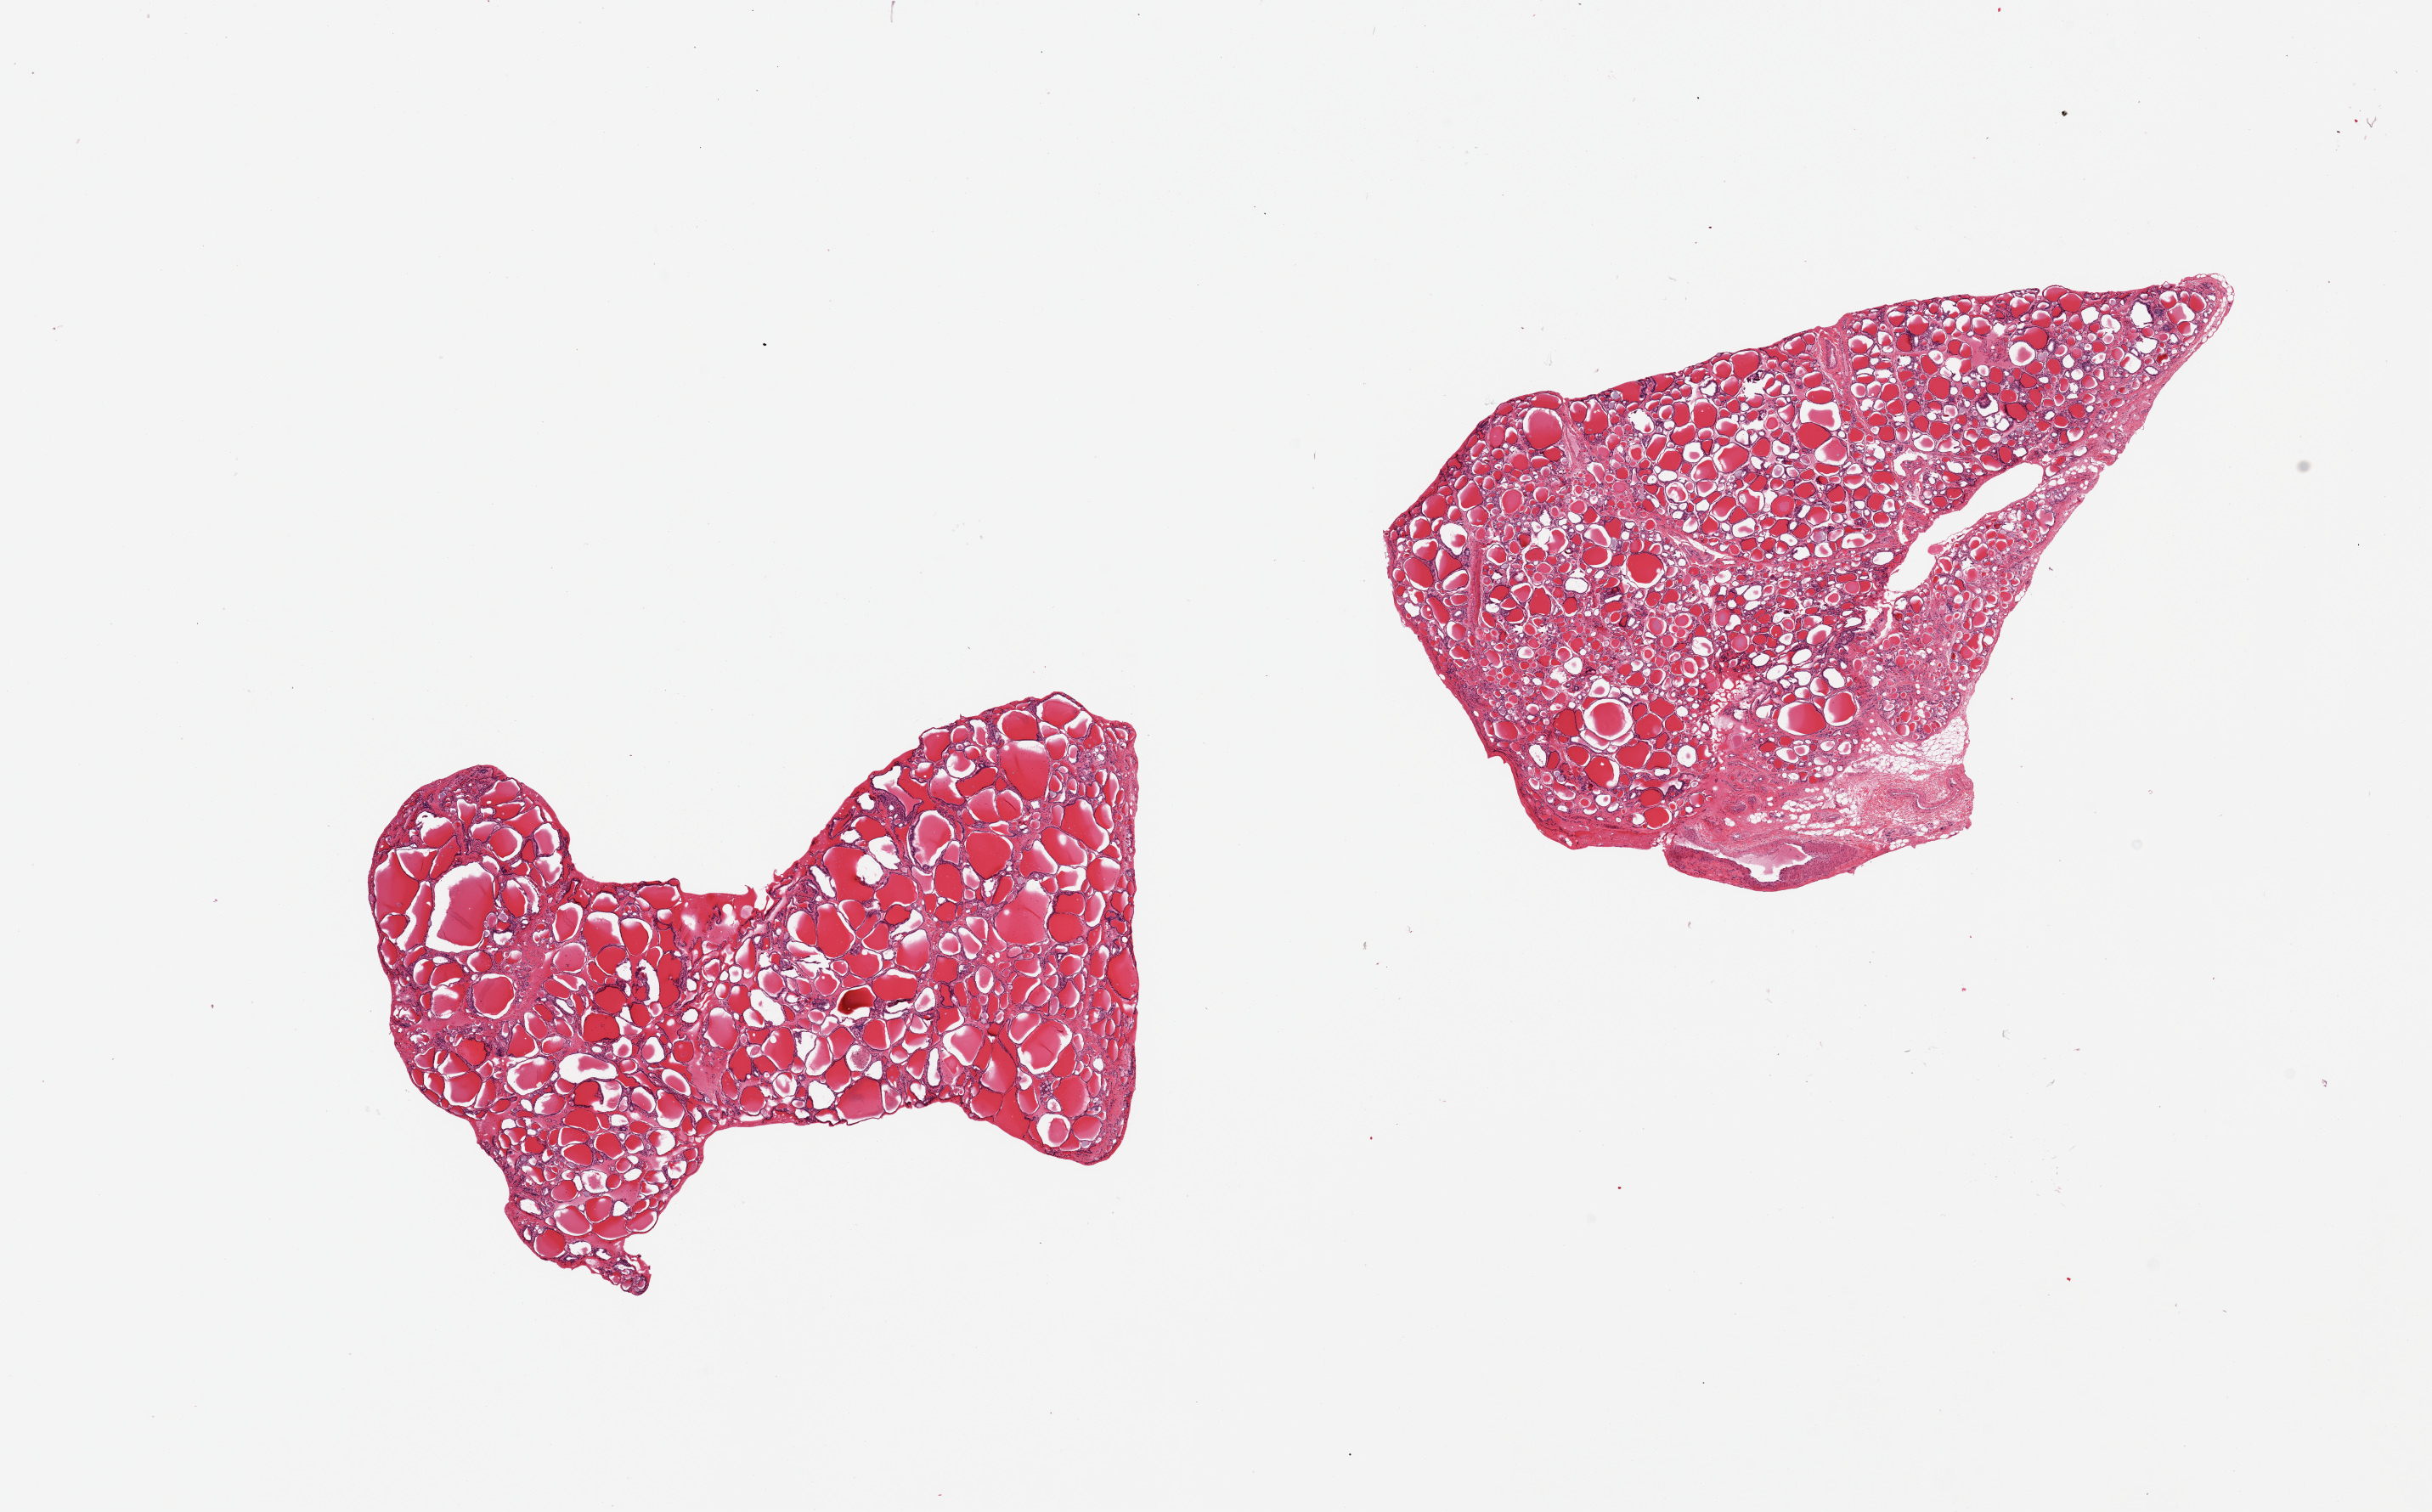
Haematoxylin and eosin whole-slide image, brightfield — low-resolution overview of the scanned area, about 22.6 x 14.1 mm (from a 20x scan). Donor sex: male.
- specimen: PAXgene-fixed paraffin-embedded (PFPE) section; section of thyroid (target tissue); tissue donor sample